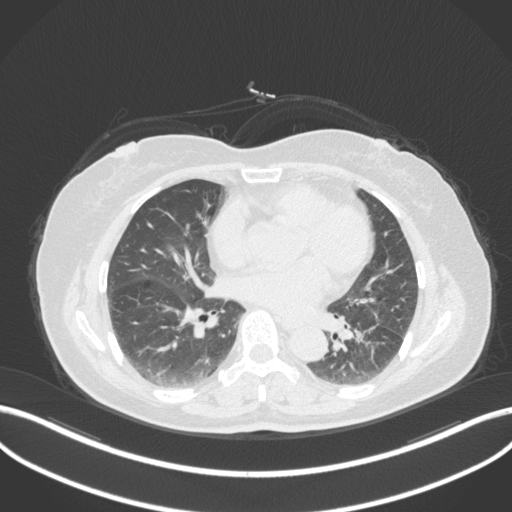
Chest CT, one axial slice. Lung window (W 1500 / L -600 HU). 512 × 512 image matrix, field of view 400 × 400 mm. Female patient, age 59 years. Case-level facts recorded for this patient, not image findings: clinical TNM (as recorded): T2a N0 M0.
Annotated regions visible in this slice (rectangle marked by the reading radiologist):
- lung tumour (recorded histology: adenocarcinoma): bounding box [x1, y1, x2, y2] px = [346, 321, 385, 369]